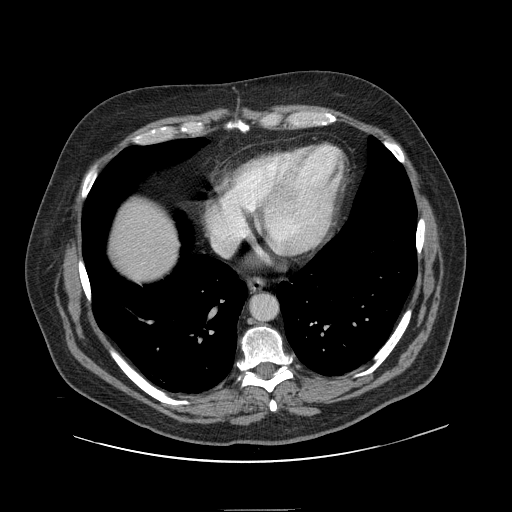
Contrast-enhanced abdominal CT, one axial slice; position 142 of 154 along the scan axis; 120 kVp; intravenous contrast given; soft-tissue window (W 400 / L 40 HU); 2.5 mm slice thickness; 512 × 512 image matrix, field of view 451 × 451 mm. Male patient, age 61 years. Case-level facts recorded for this patient, not image findings: diagnosis: colorectal cancer liver metastases, imaged before liver resection; multiple liver metastases: yes; largest metastasis: 2.6 cm; disease in both lobes: yes.
Outlined on this slice (expert manual segmentation):
- liver: box from (x=111, y=201) to (x=178, y=280) px
- planned liver remnant (the part of the liver to remain after resection): (x=111, y=201)–(x=178, y=281)